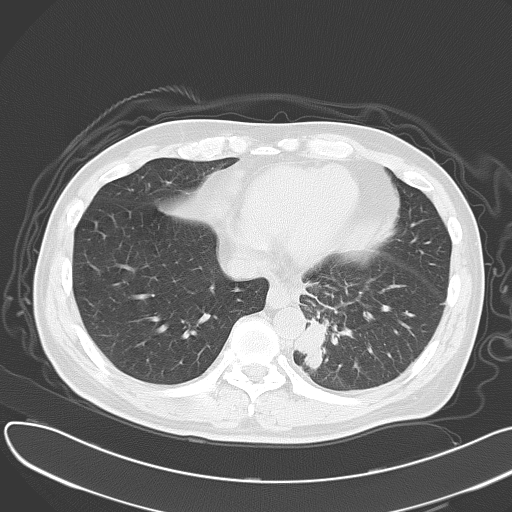
Chest CT, one axial slice; slice 15 of 55 in the series (ordered by position); reconstruction kernel B70f; lung window (W 1500 / L -600 HU); 5 mm slice thickness; 512 × 512 image matrix, field of view 376 × 376 mm. Patient: male, 55 years. Case-level facts recorded for this patient, not image findings: clinical TNM (as recorded): T2 N3 M0.
Outlined on this slice (bounding box drawn by a radiologist):
- lung tumour (recorded histology: small cell carcinoma): bounding box [x1, y1, x2, y2] px = [298, 316, 332, 365]